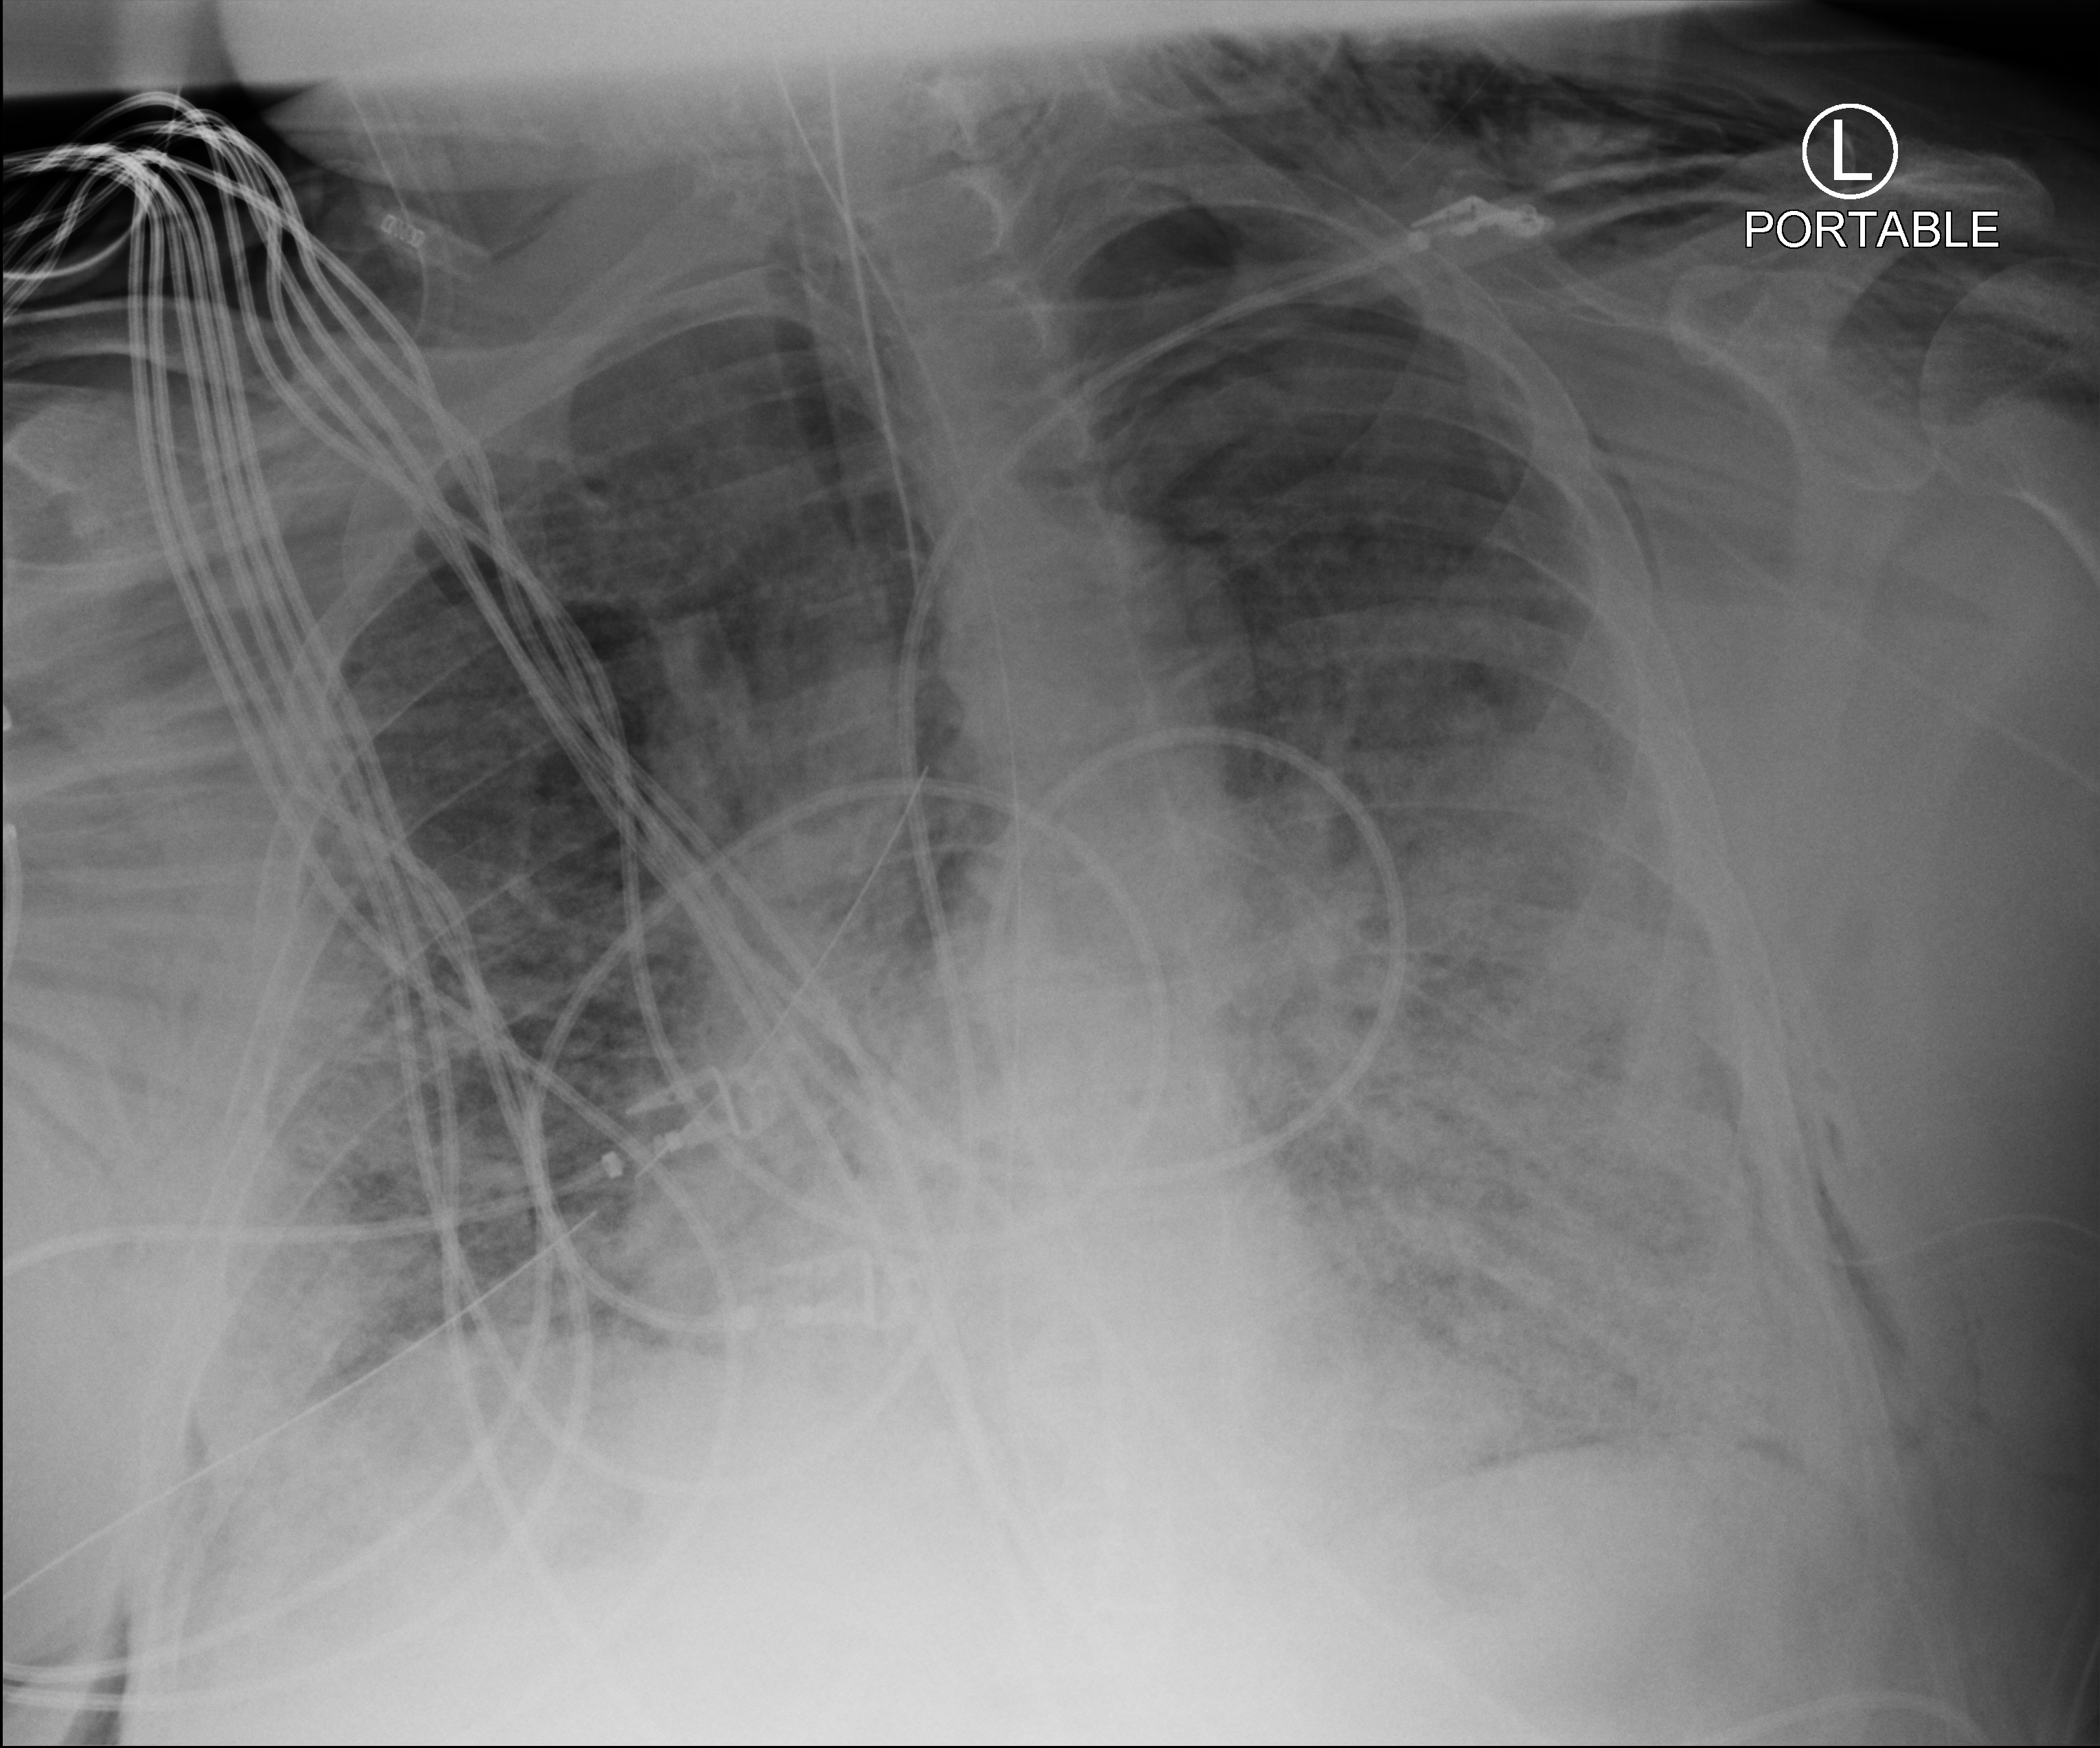
Chest X-ray (portable); anteroposterior (AP) projection. Adult patient hospitalised with COVID-19, age 18–59 years.
Hospital-stay facts (about this admission, not read from this image; timing relative to this image not recorded):
- hypertension (admission record): yes
- admitted to intensive care during this hospital stay: yes
- mechanically ventilated during this hospital stay: yes